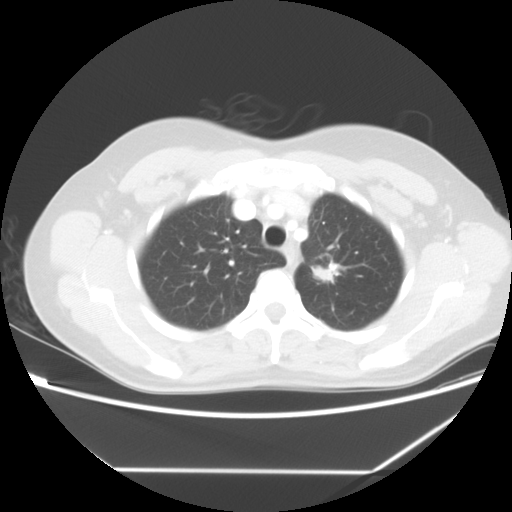
Chest CT, one axial slice. Position 47 of 60 along the scan axis. Reconstruction kernel STANDARD. 140 kVp. Lung window (W 1500 / L -600 HU). 5 mm slice thickness. 512 × 512 image matrix, field of view 367 × 367 mm. Patient: female, 43 years. Case-level facts recorded for this patient, not image findings: clinical TNM (as recorded): T1c N0 M1b.
Structures marked on this image (rectangle marked by the reading radiologist):
- lung tumour (recorded histology: adenocarcinoma): bounding box (x1, y1, x2, y2) in pixels: (313, 262, 336, 287)